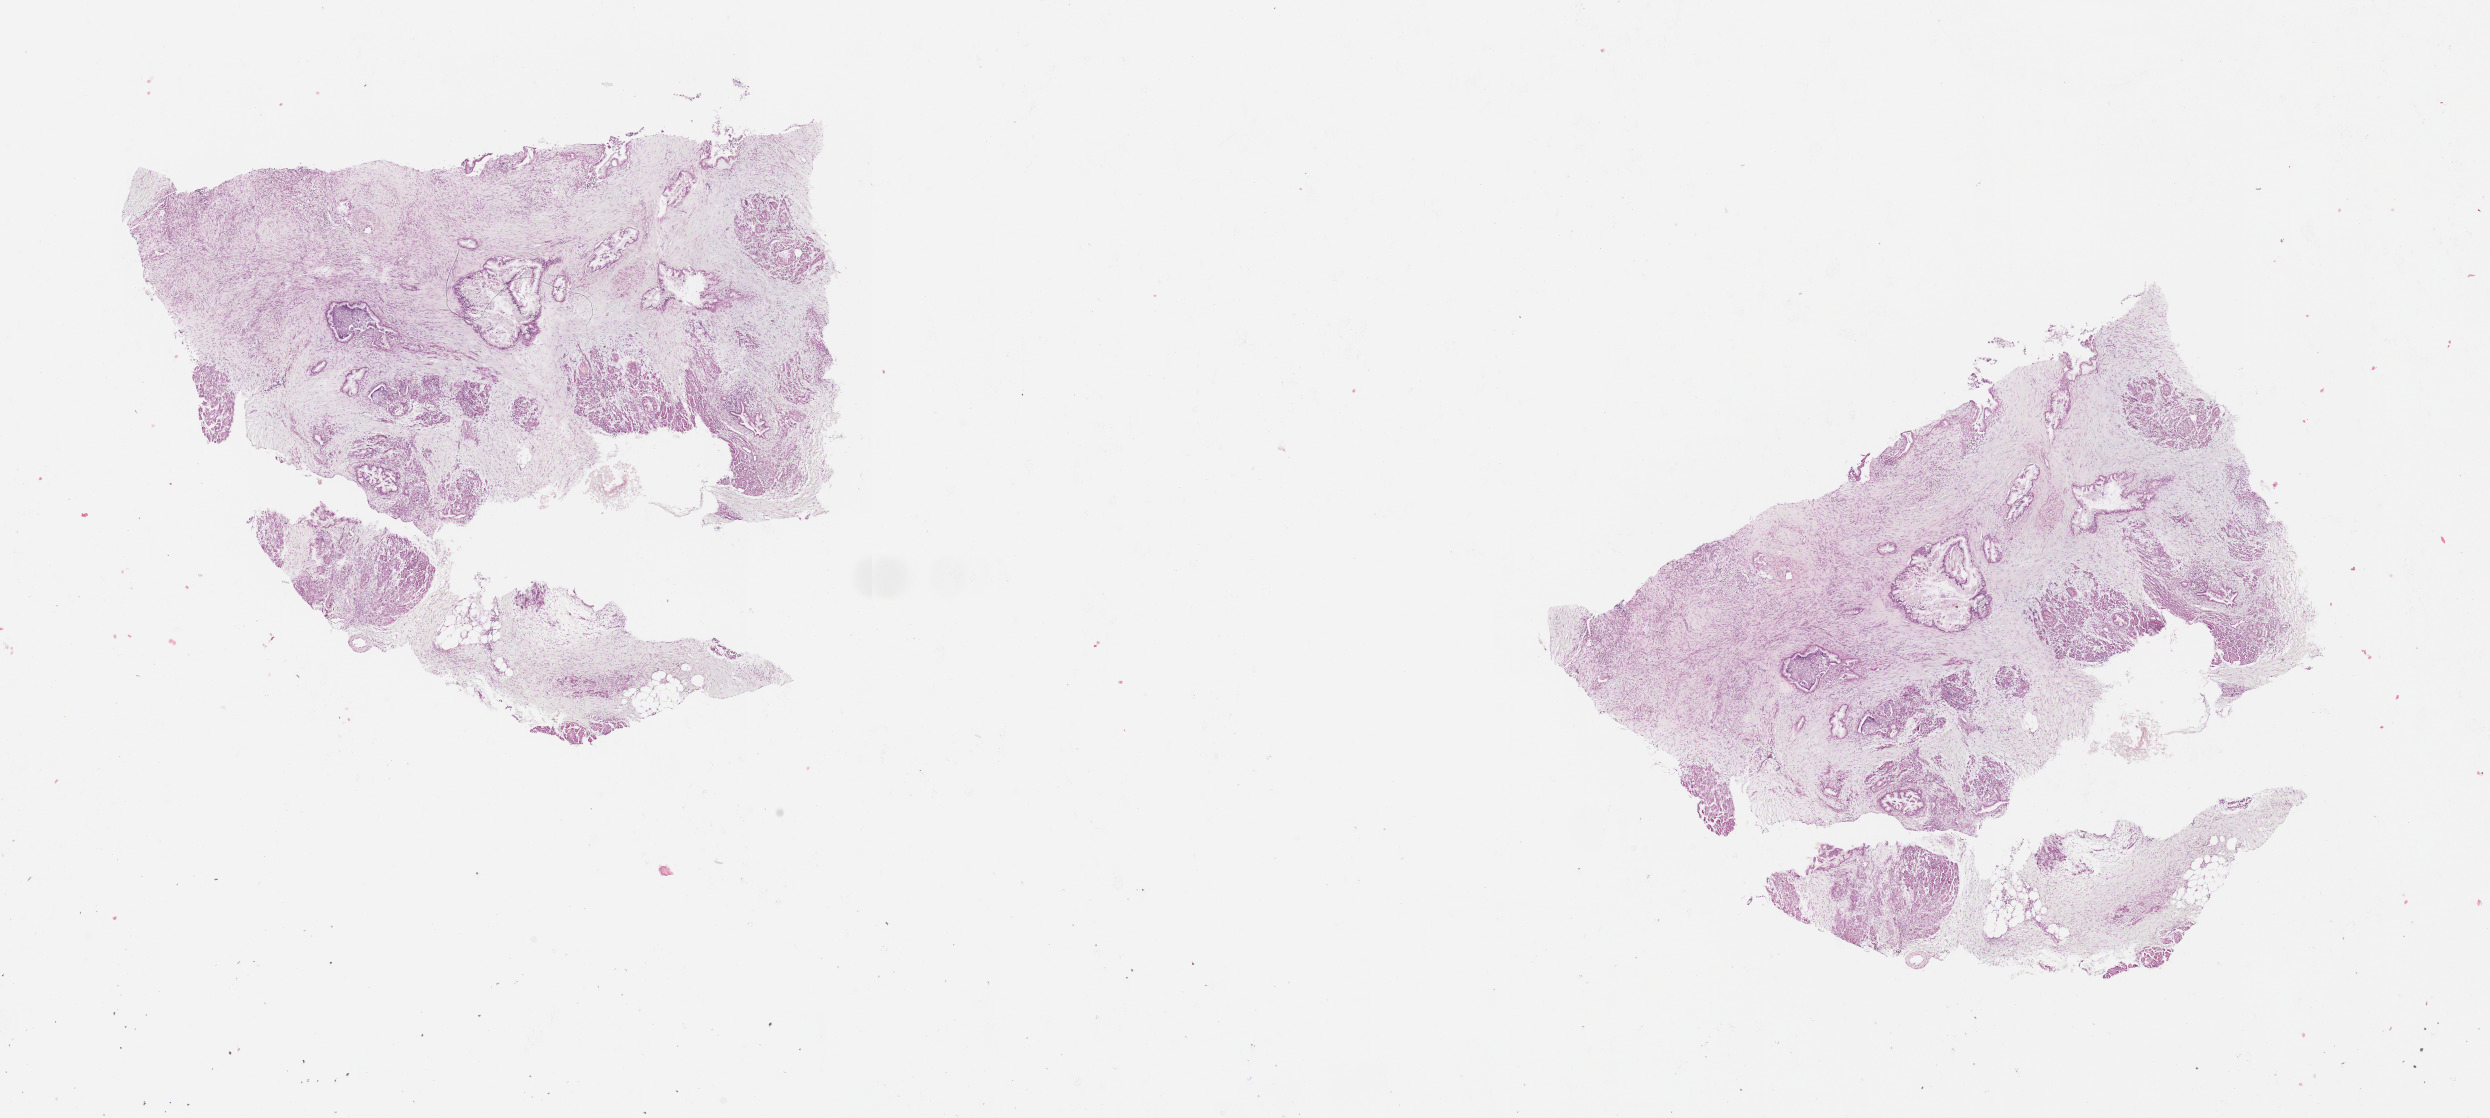
Whole-slide histology image, H&E-stained, low-resolution overview of the scanned area, about 20.0 x 9.0 mm (slide scanned at 20x). Tumour tissue sample, sampled site: pancreas. Male, 60 y/o. Histologic grade: G2 (moderately differentiated). Composition of this section per pathologist review: tumour nuclei 10%, necrosis 3%.
Diagnosis: Infiltrating duct carcinoma, NOS. AJCC pathologic stage: III. Primary tumour site (as recorded): head.